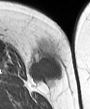
MRI of an extremity soft-tissue mass, one axial slice; position 11 of 45 along the scan axis; MR volume resampled by the dataset authors to the PET/CT grid (not the native acquisition matrix); 3.27 mm slice thickness; 90 × 109 image matrix, field of view 88 × 106 mm. Female patient. From the clinical record (not read from this slice): histological type: leiomyosarcoma; grade: intermediate; site of the primary tumour: parascapusular.
Outlined on this slice (expert contour drawn on MRI and transferred to this co-registered scan by the dataset authors):
- gross tumour volume including surrounding oedema: box from (x=30, y=43) to (x=63, y=83) px
- gross tumour volume (mass): (x=30, y=55)–(x=63, y=81)